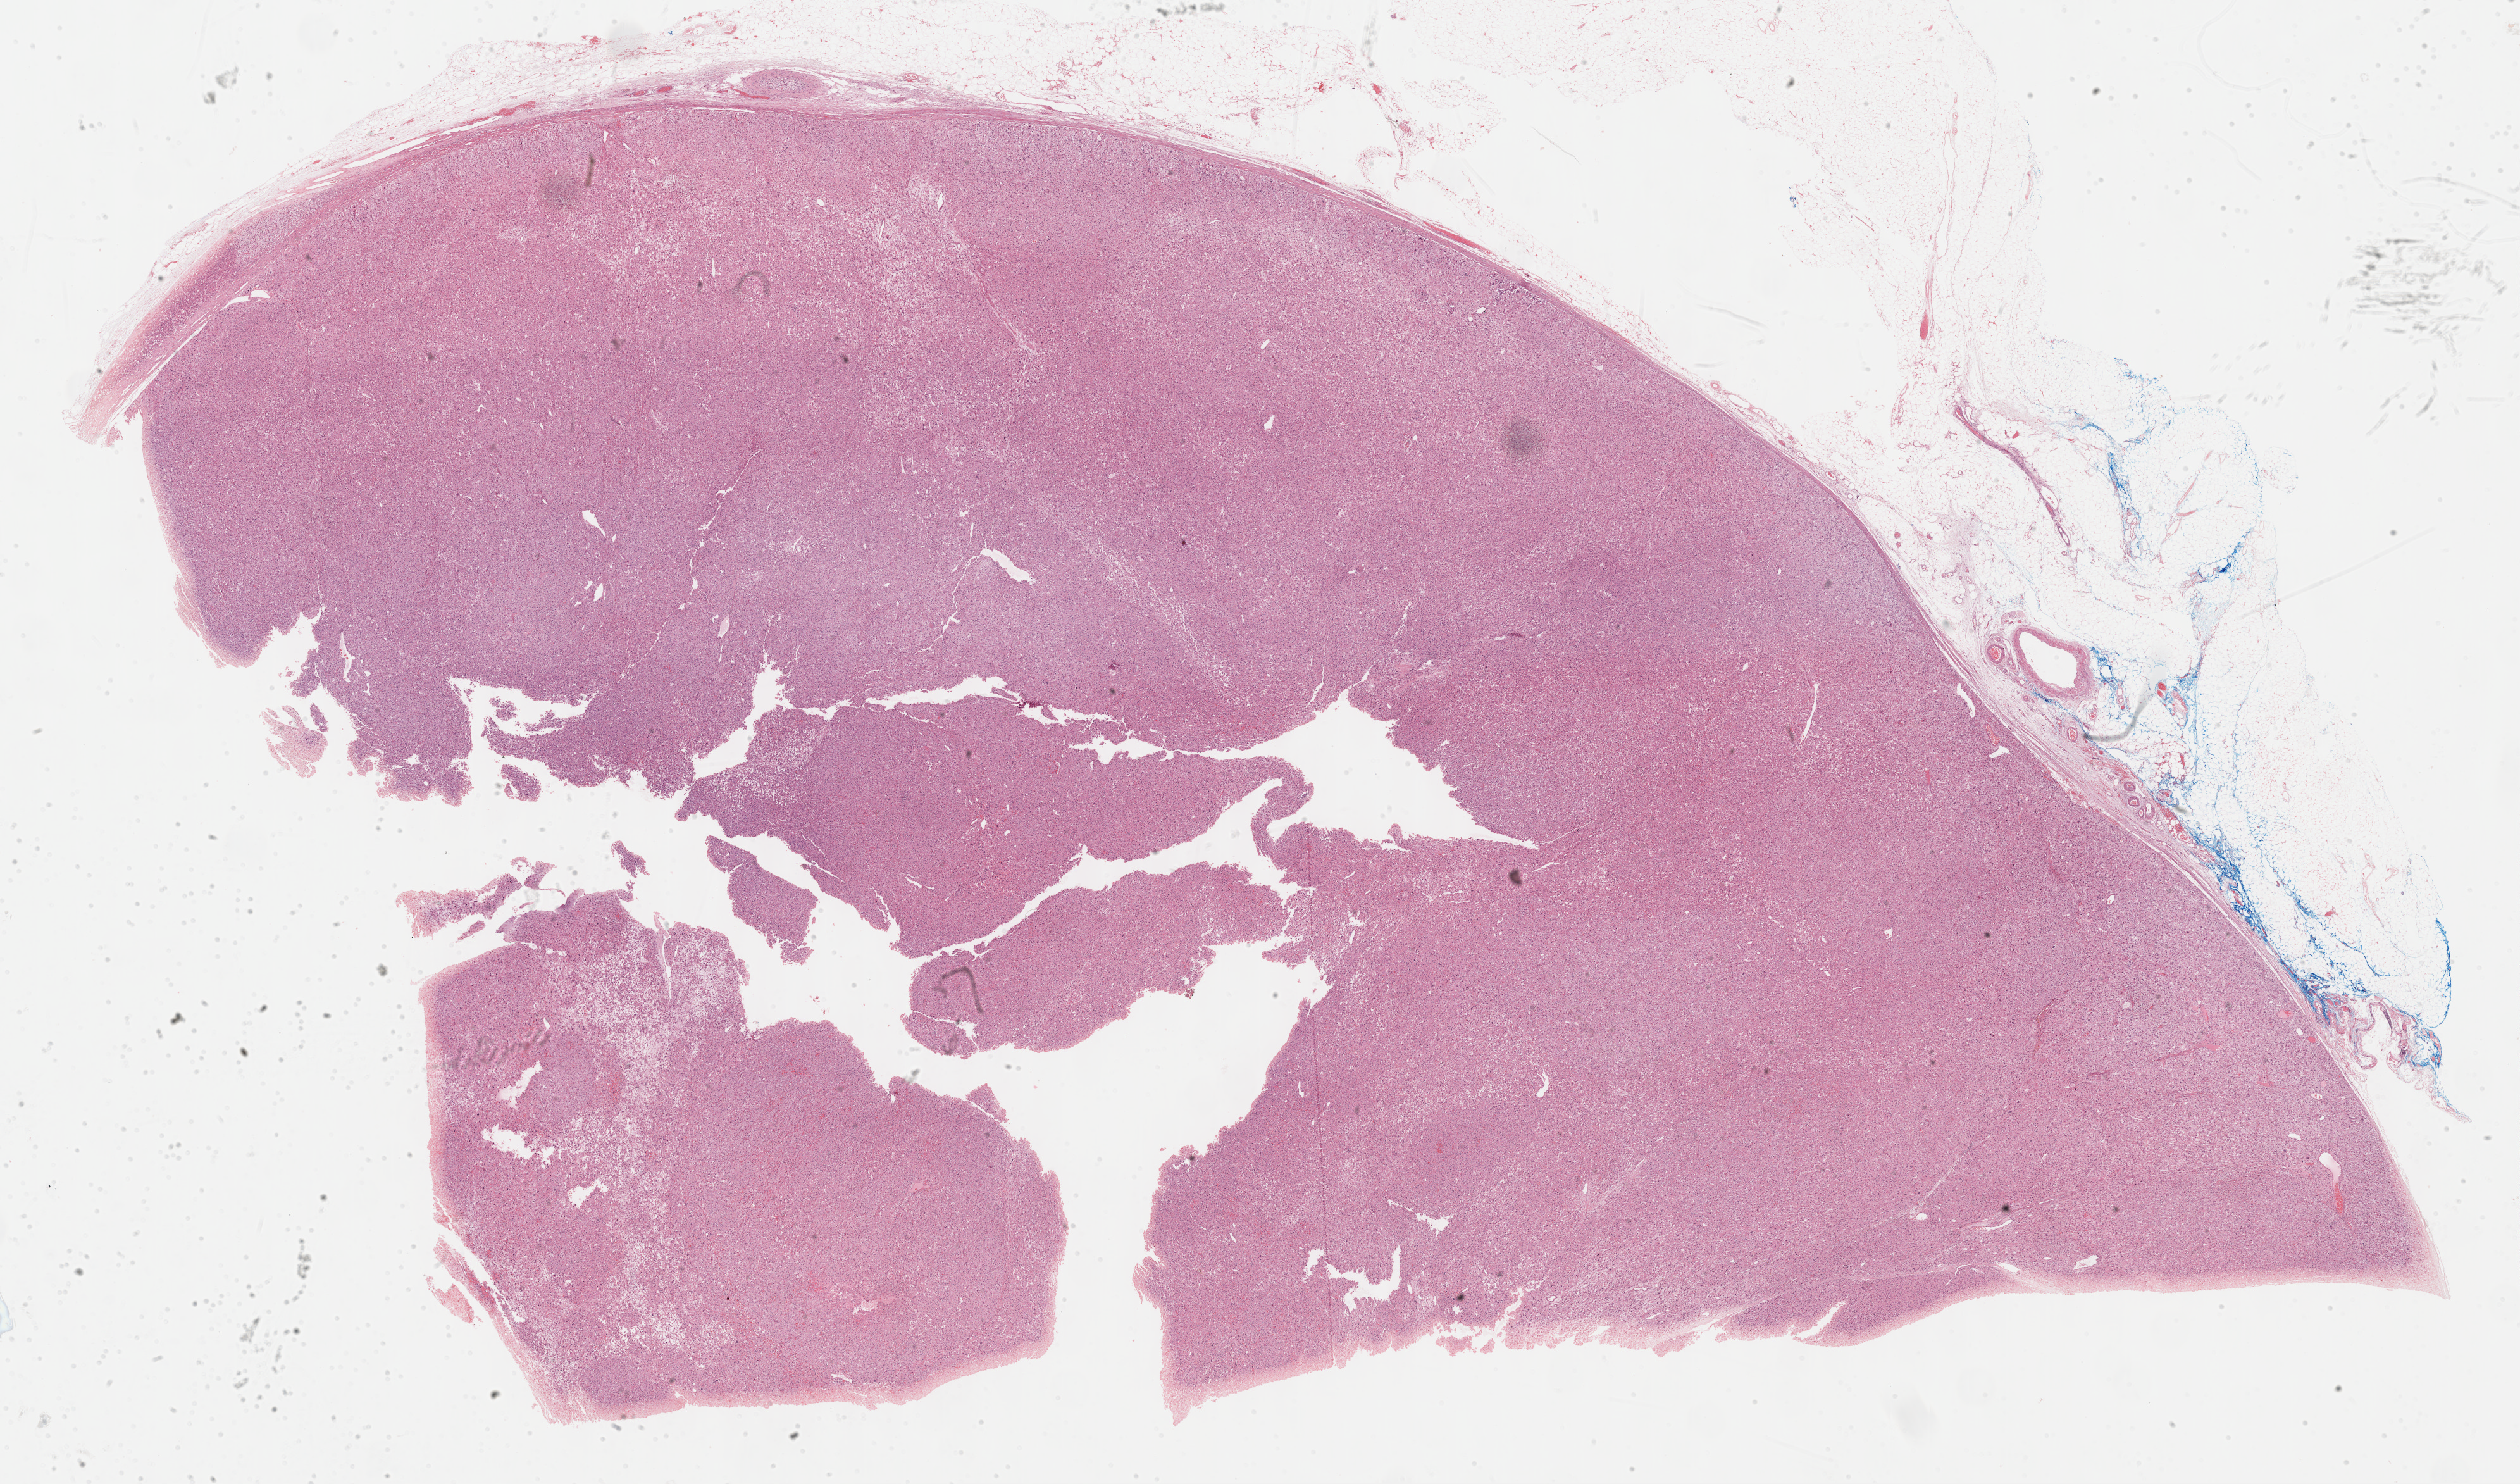
H&E-stained whole-slide image, whole scanned area (about 32.2 x 19.0 mm, slide scanned at 40x) shown as a low-resolution overview. Formalin-fixed paraffin-embedded (FFPE) diagnostic section. Adrenal cortex, primary tumour sample. Male, age 45 years at initial diagnosis.
Laterality: left. Pathologic diagnosis: Adrenal cortical carcinoma (cortex of adrenal gland).